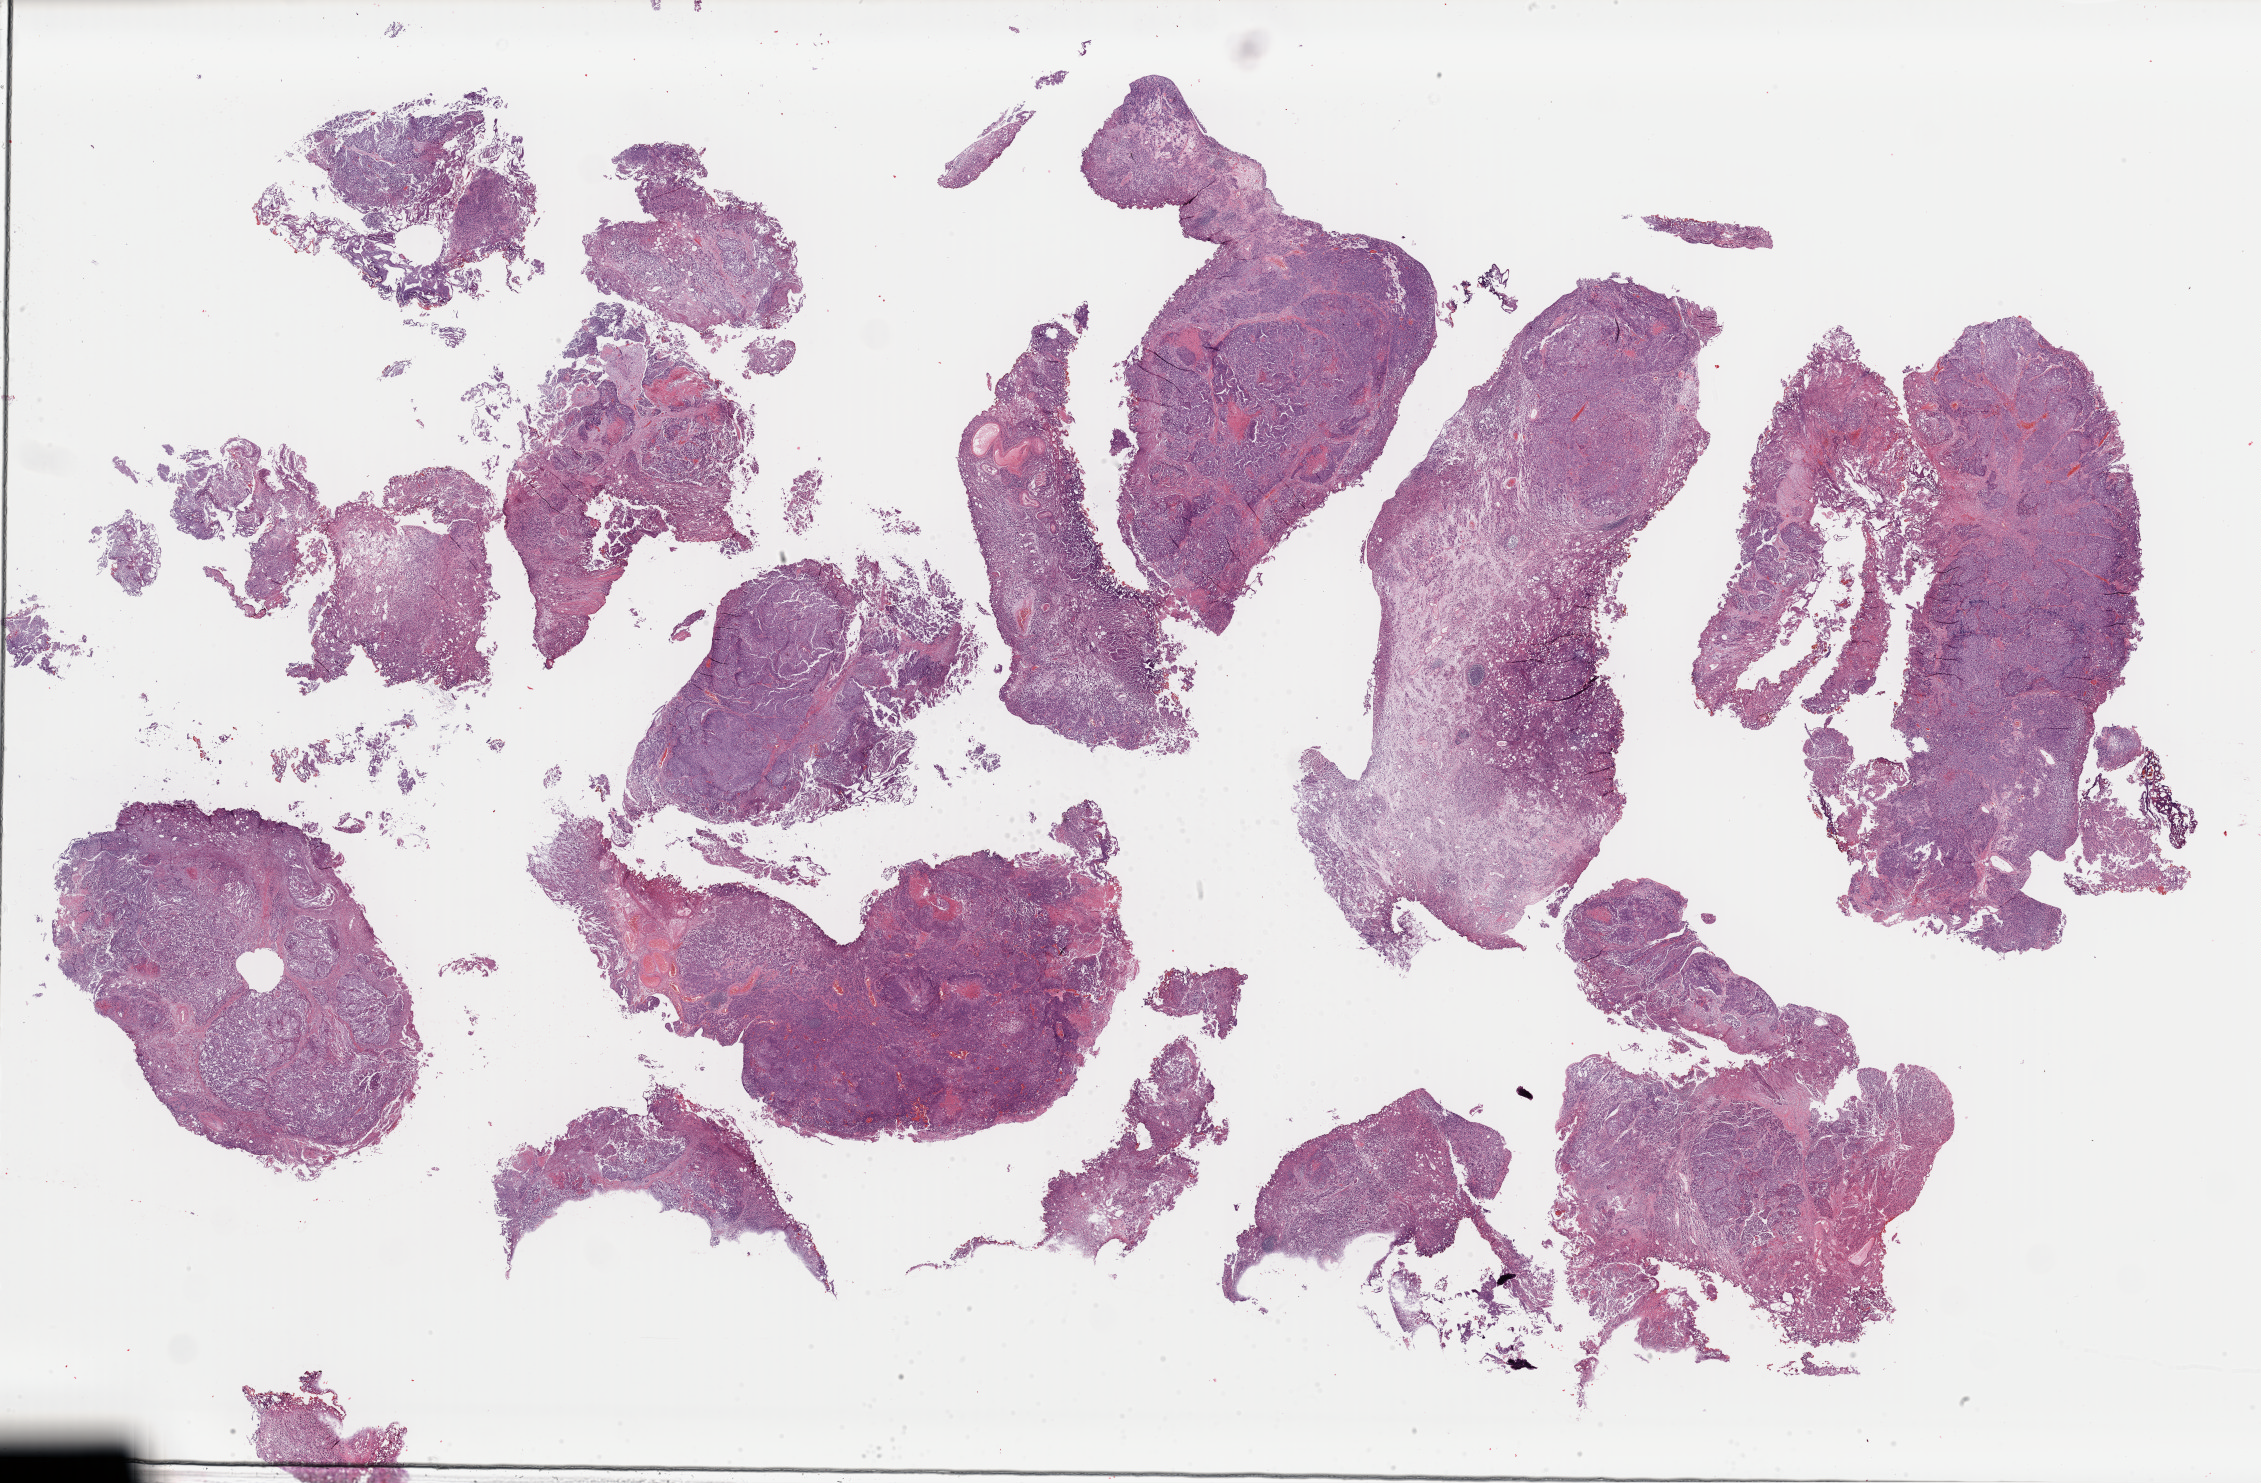
Digitized Hematoxylin and eosin (H&E) stained tissue section (whole slide), a low-resolution overview of the entire scanned area, about 35.7 x 23.4 mm; FFPE section; bladder, primary tumour sample. Male, age 64 years at initial diagnosis. Histologic grade: high grade.
Histologic diagnosis: Transitional cell carcinoma. AJCC pathologic stage: IV (7th edition). TNM: T4b N2 MX.